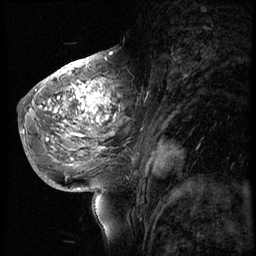
Breast MRI (dynamic contrast-enhanced), one sagittal slice. Slice 29 of 56 in the series (ordered by position). 4 images stored at this slice position (order not interpretable as contrast timing). 1.5 T. TE 4.2 ms, TR 8.9 ms. 2.5 mm slice thickness. 256 × 256 image matrix, field of view 220 × 220 mm. Patient: female, 51 years. Case-level facts recorded for this patient, not image findings: setting: breast cancer imaged before/during neoadjuvant chemotherapy; receptor status: triple-negative.
Annotated regions visible in this slice (semi-automatic segmentation, software-assisted and operator-edited):
- analysis volume of interest (the breast-tissue region the enhancement analysis was run in; not a lesion): box from (x=30, y=70) to (x=150, y=173) px
- tumour enhancement mask (voxels above the 140 % enhancement threshold inside the analysis volume of interest): (x=46, y=70)–(x=113, y=137)